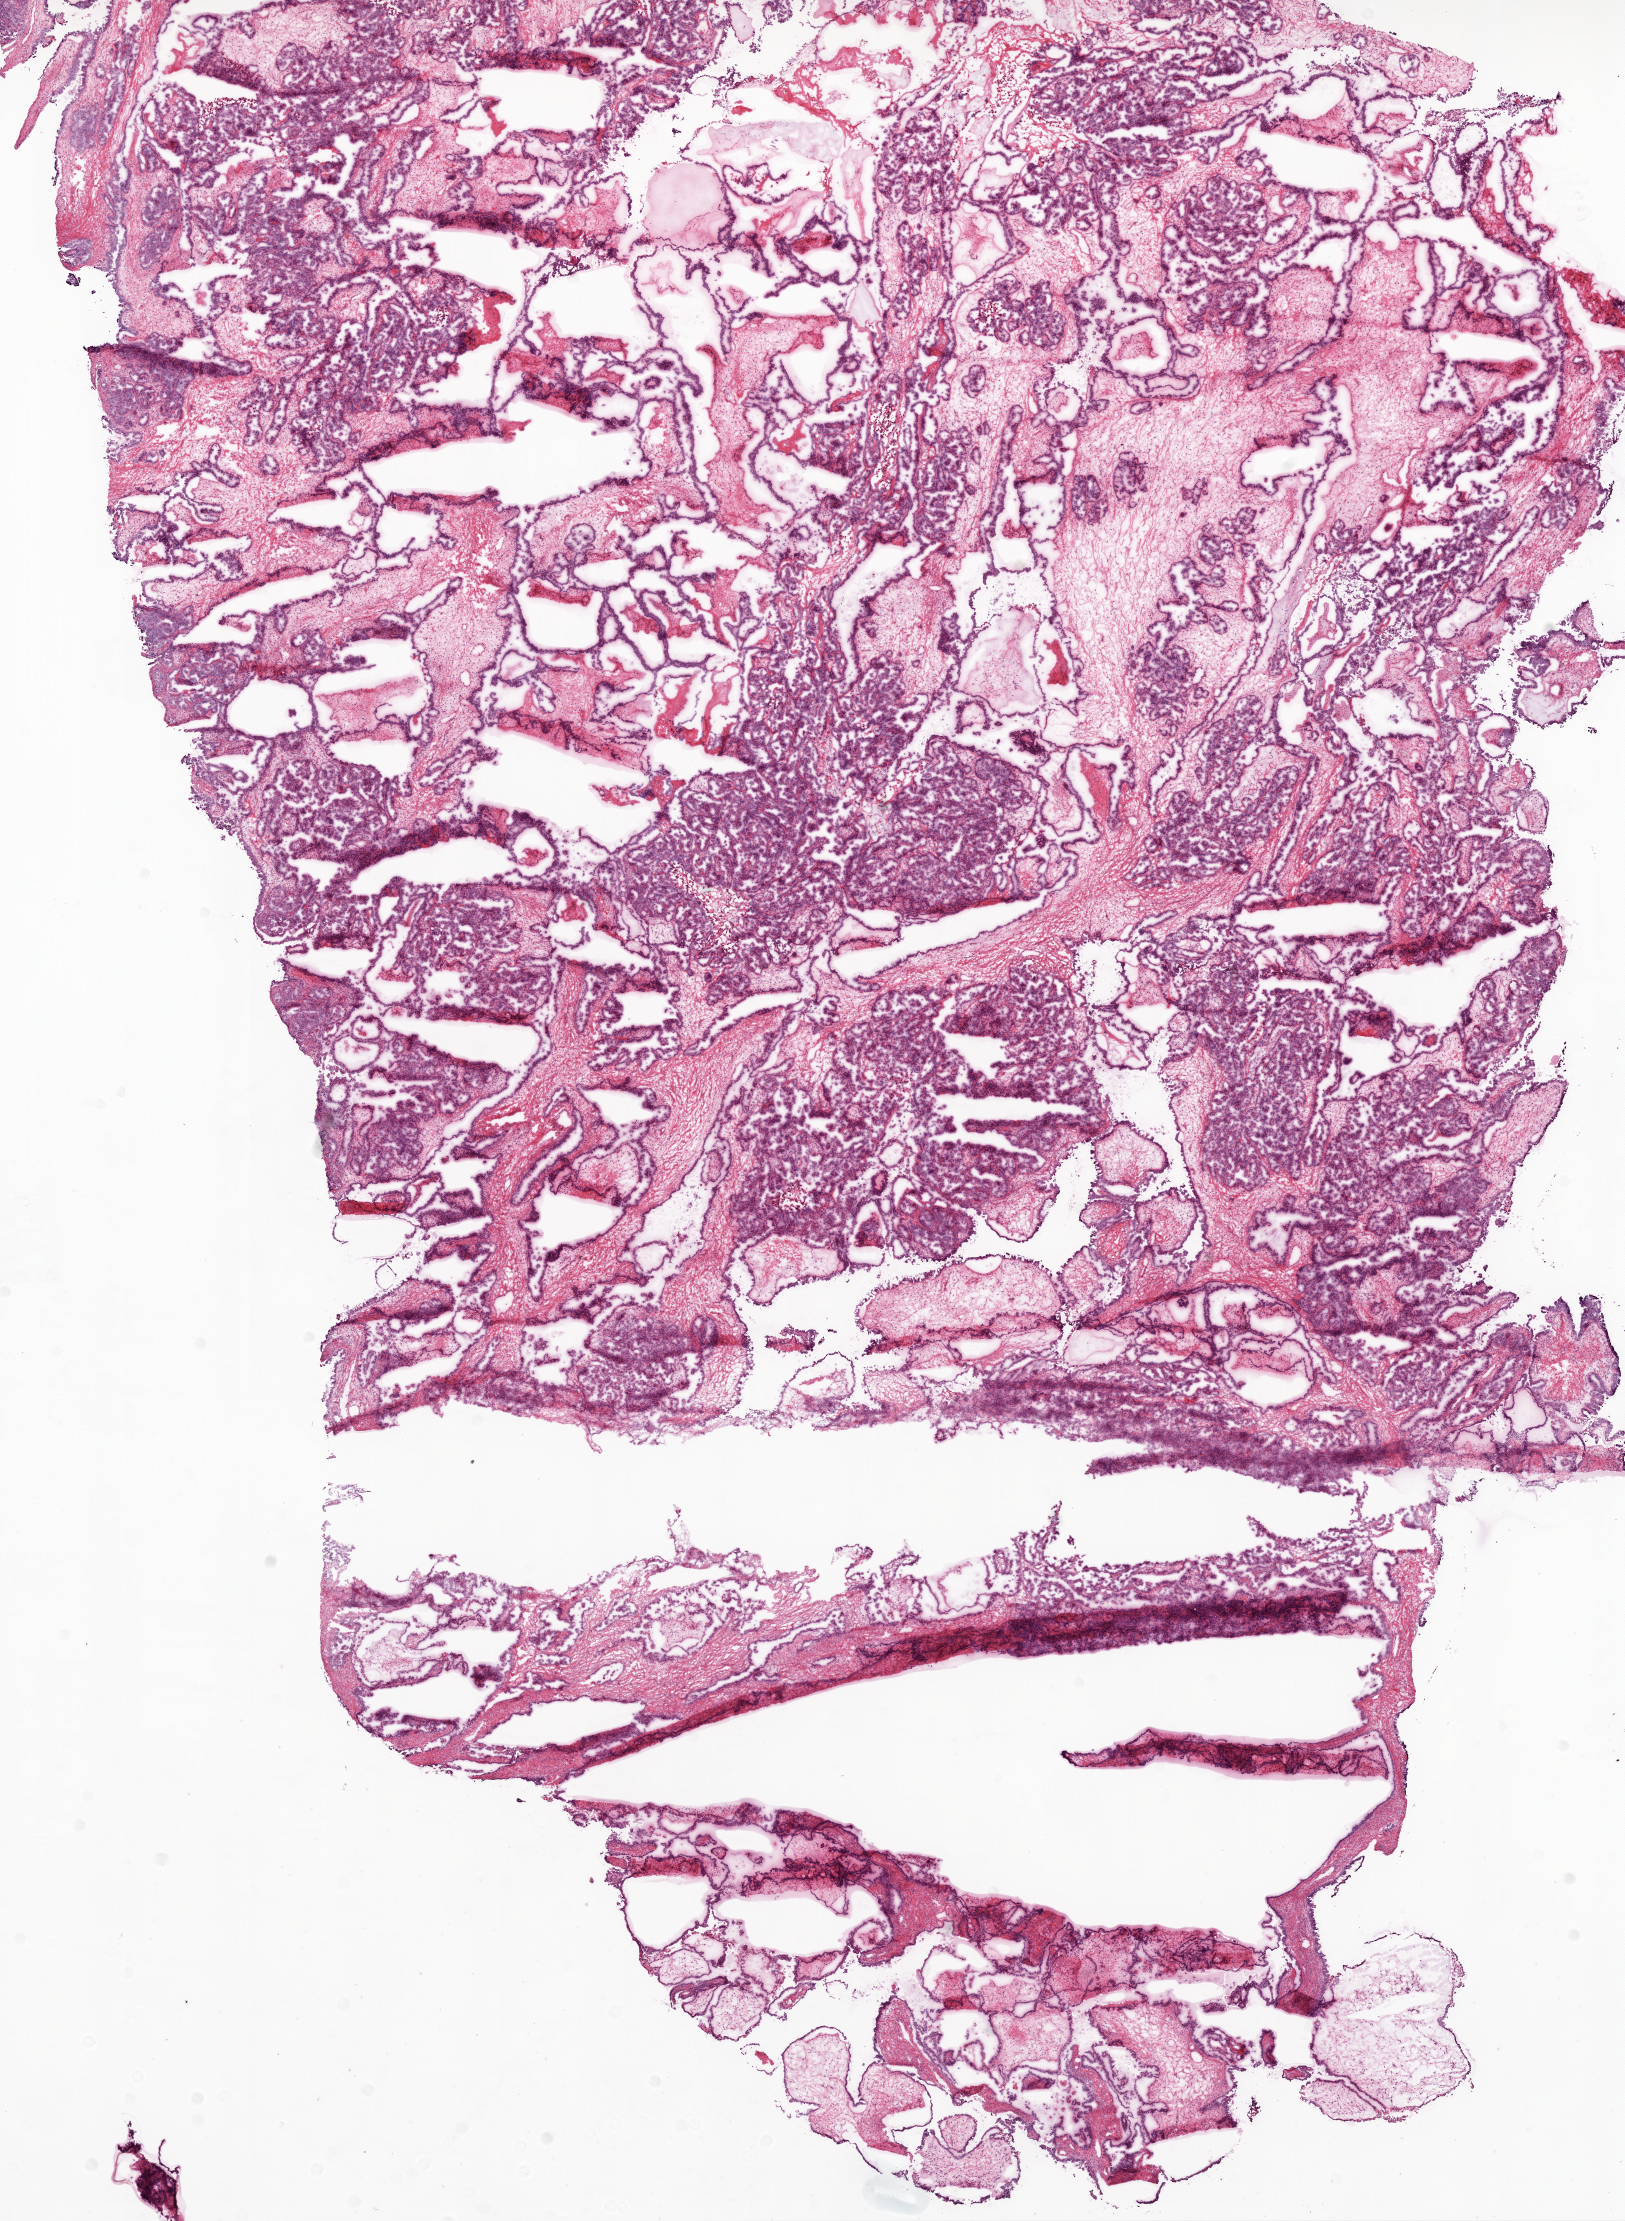
Hematoxylin and eosin (H&E) stained whole-slide image — a low-resolution overview of the entire scanned area, about 13.0 x 17.8 mm. Frozen section. Sample: primary tumour, ovary. Female patient; age at initial diagnosis 75 years. Histologic grade: G3 (poorly differentiated). Pathologist review of this section (percent, as recorded): tumour cells 84%, tumour nuclei 85%, normal cells 0%, stromal cells 15%, necrosis 1%.
• FIGO stage: IIIC
• histologic diagnosis: Serous cystadenocarcinoma, NOS